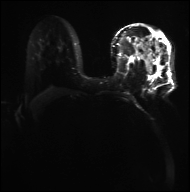
Breast MRI, one axial slice. Slice 18 of 36 in the series (ordered by position). Diffusion-weighted series; image 2 of 4 stored at this slice position (different b-values; order by instance number). 3 T. 190 × 192 image matrix, field of view 317 × 320 mm. Female patient.
Structures marked on this image (manually delineated by an expert):
- tumour on diffusion-weighted imaging: box from (x=6, y=43) to (x=70, y=76) px